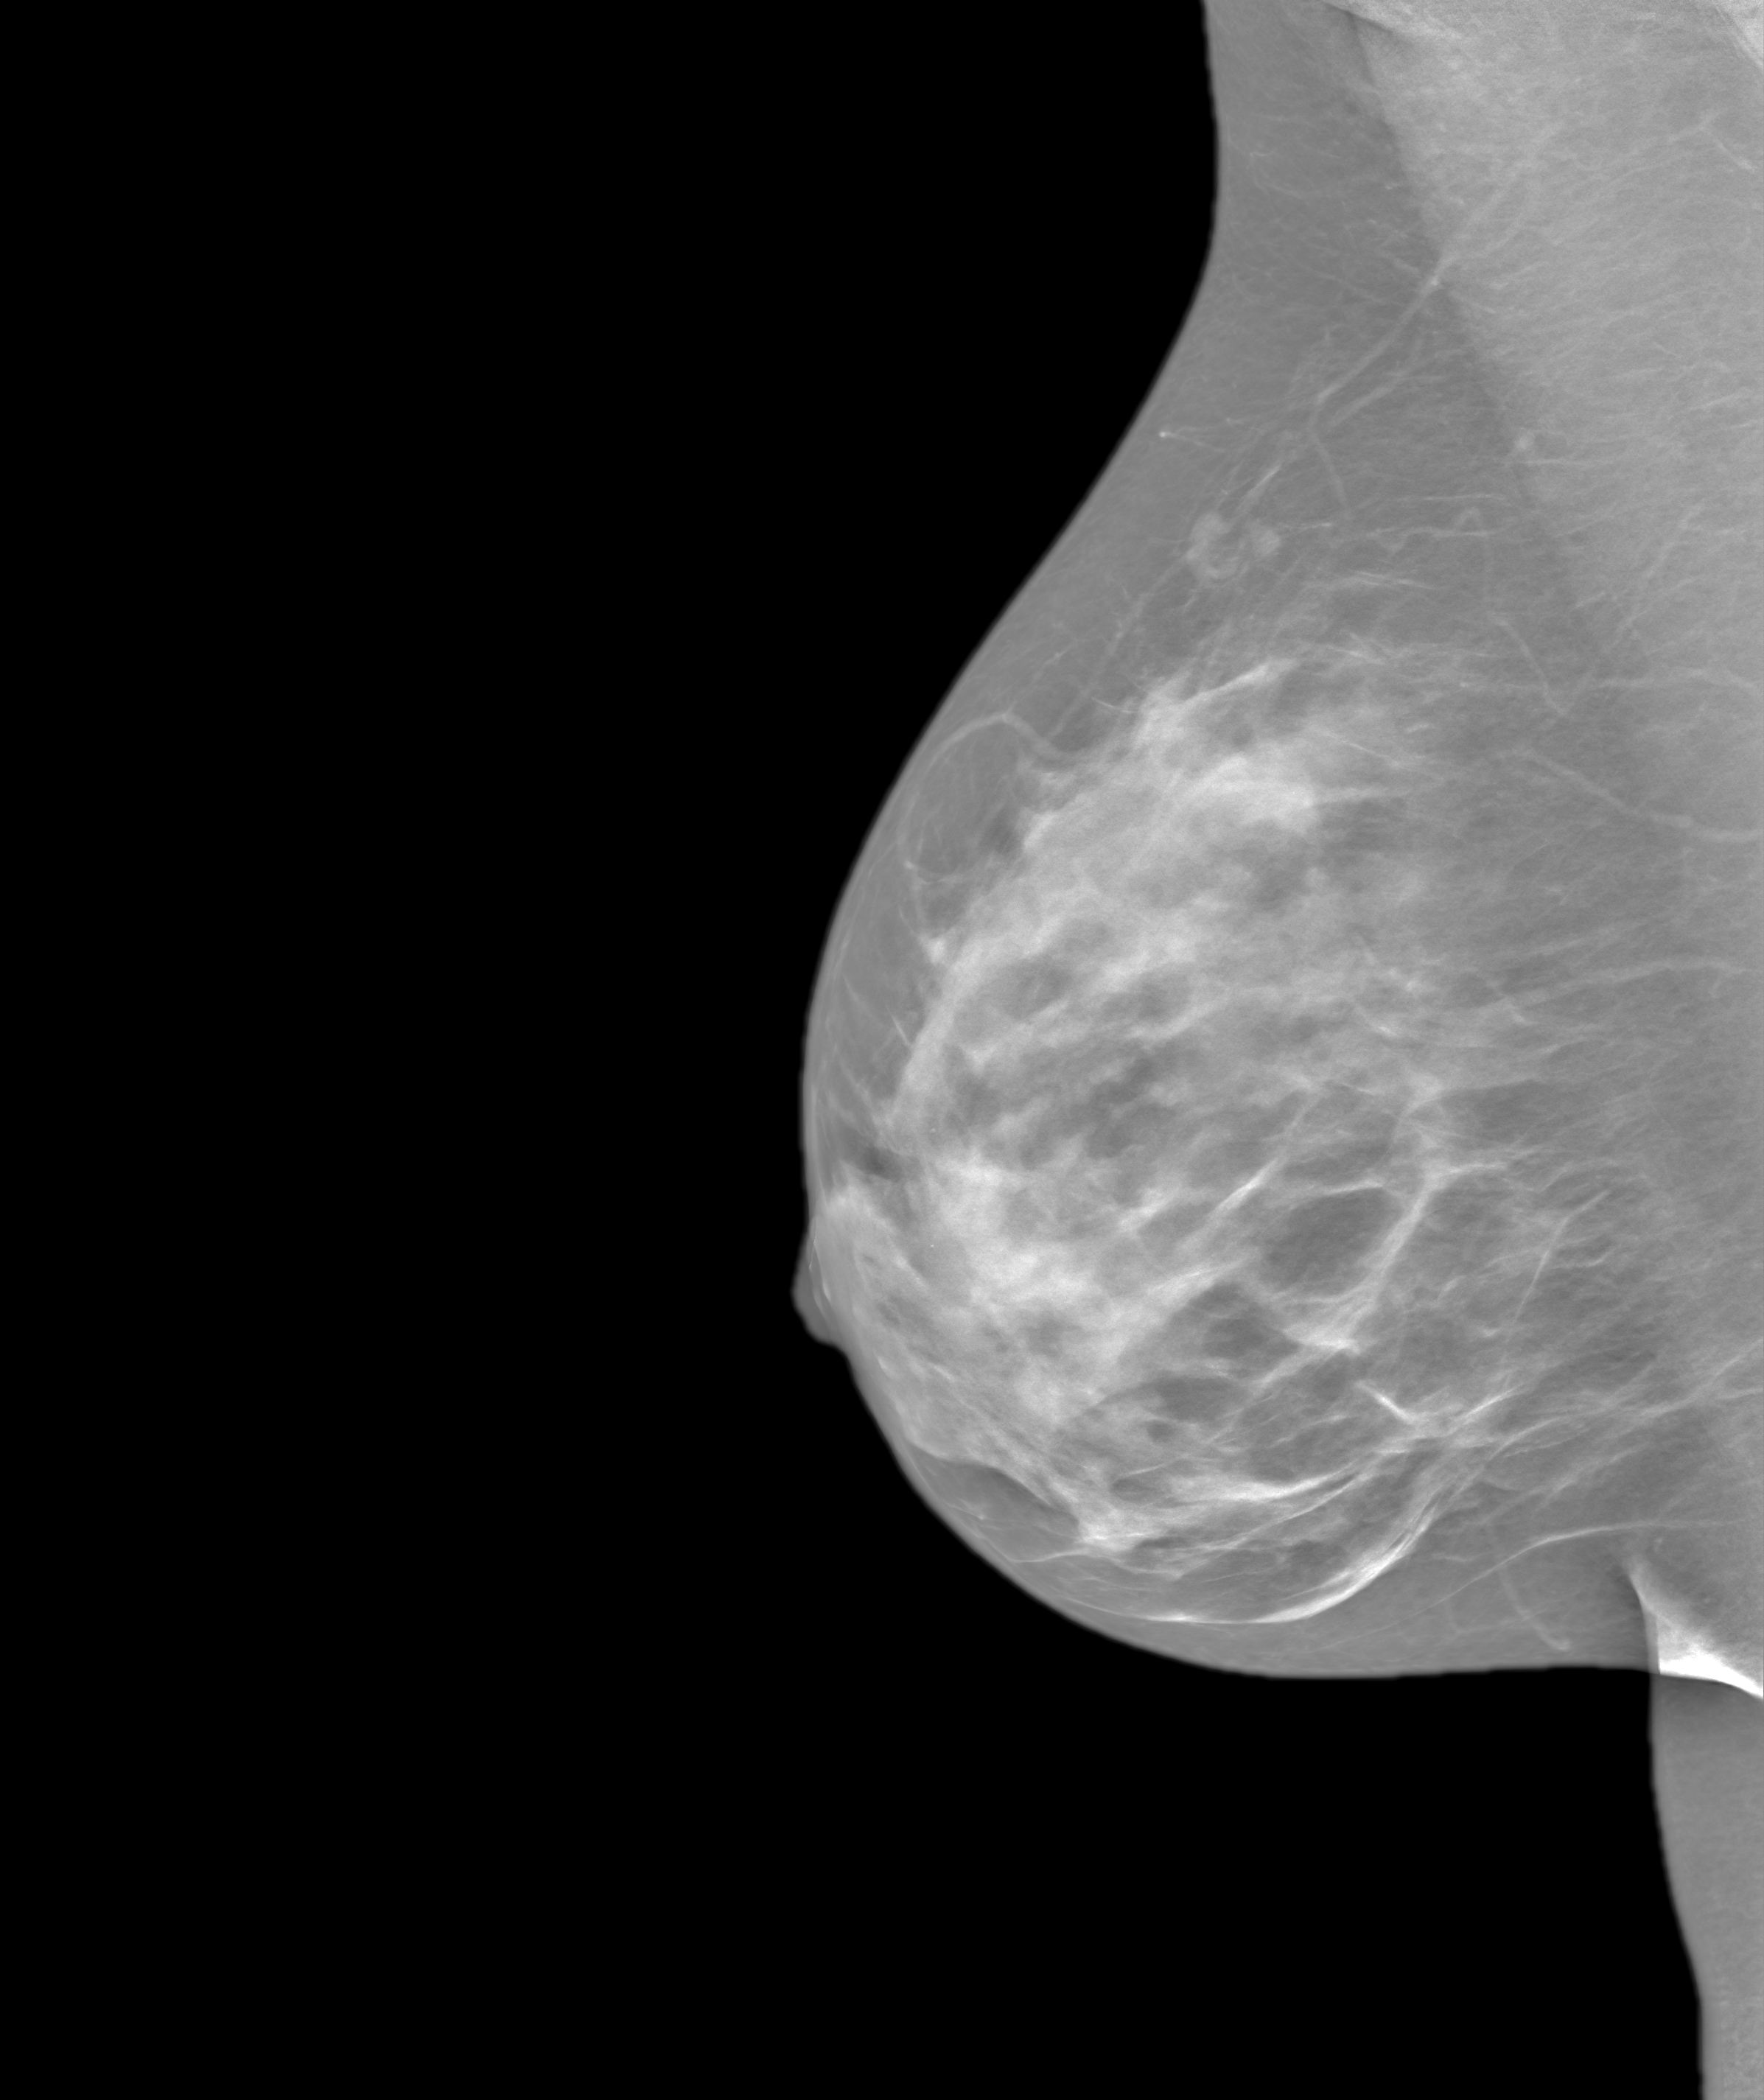
Annual screening mammography examination. Female patient, age 47 years.
Image type: synthesized 2-D view from tomosynthesis. Breast: right. Projection: MLO view.